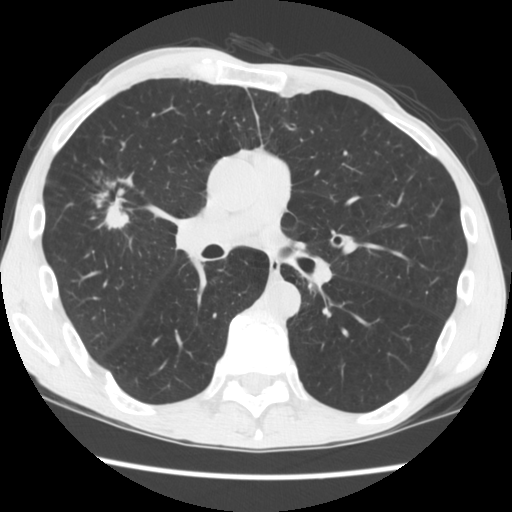
Low-dose screening chest CT, one axial slice; slice 96 of 181 in the series (ordered by position); reconstruction kernel STANDARD; 120 kVp; lung window (W 1500 / L -600 HU); 2.5 mm slice thickness; 512 × 512 image matrix, field of view 330 × 330 mm.
Structures marked on this image (outlined manually by an expert reader):
- lesion 1 (tumor, upper lobe of right lung): bounding box <96,182,130,230> (left, top, right, bottom; pixels)